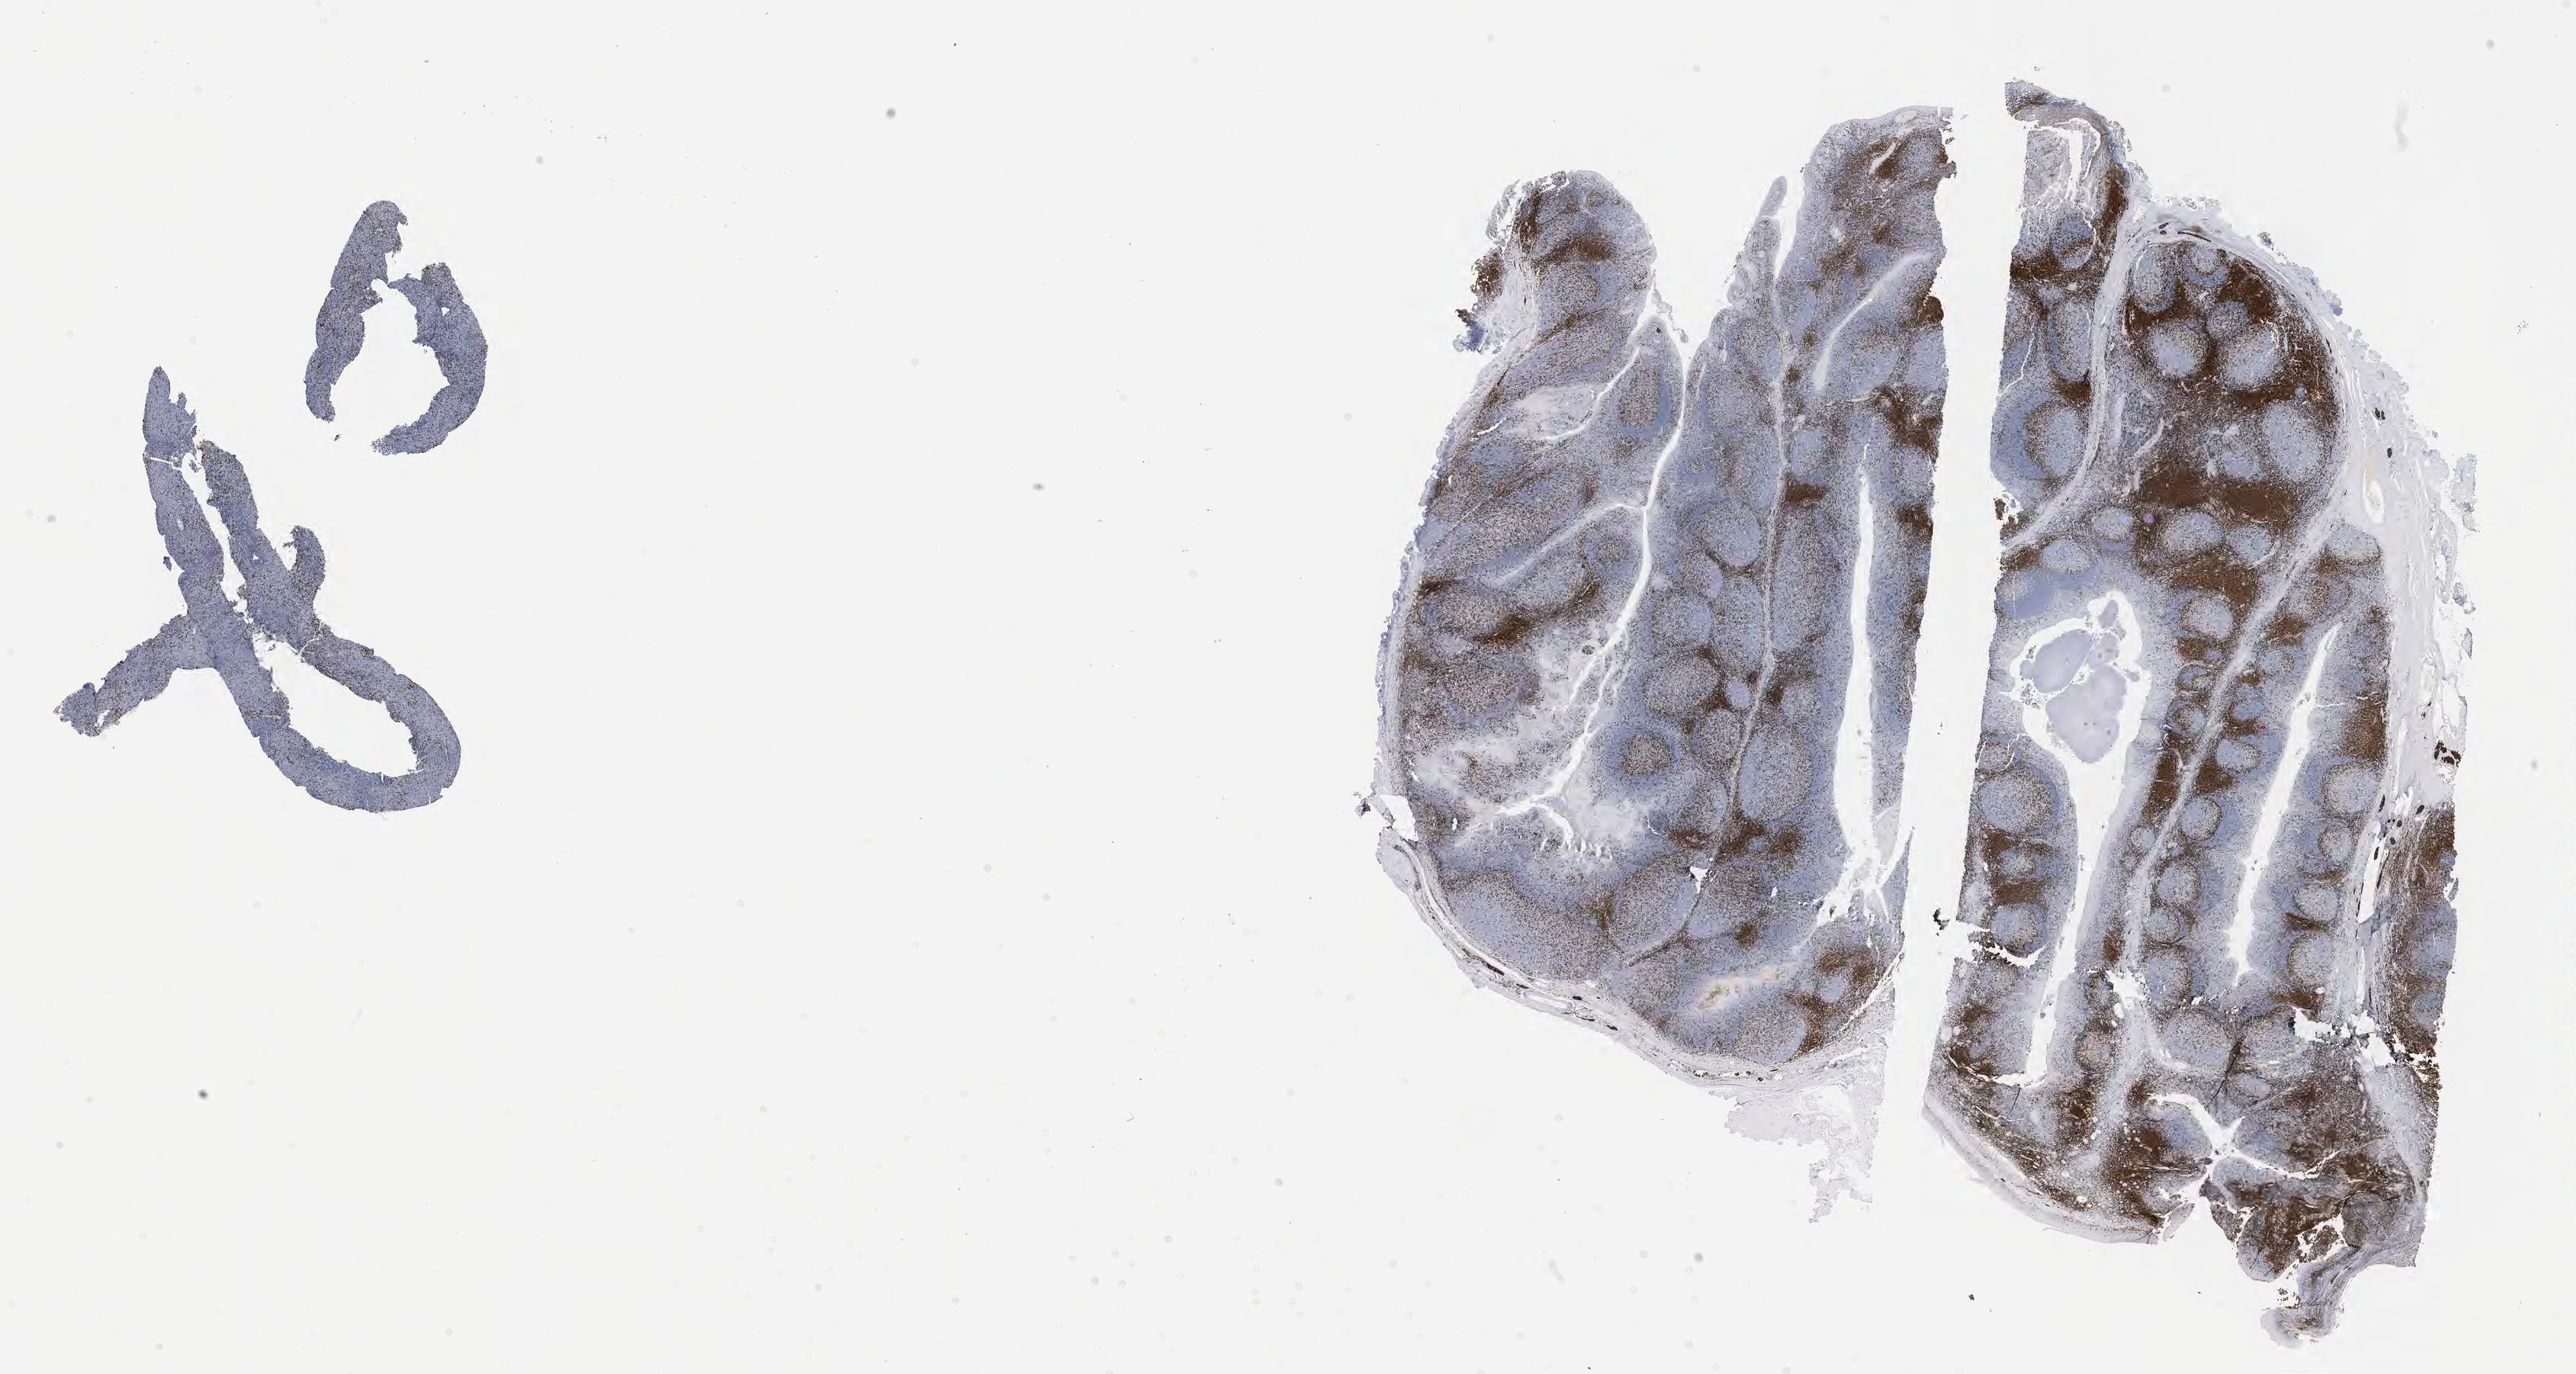
IHC for CD3, whole-slide image — shown as a low-resolution overview of the whole scanned area (about 28.7 x 15.3 mm). Patient male; 52 years old.
* specimen: tumor tissue; anatomic site: liver